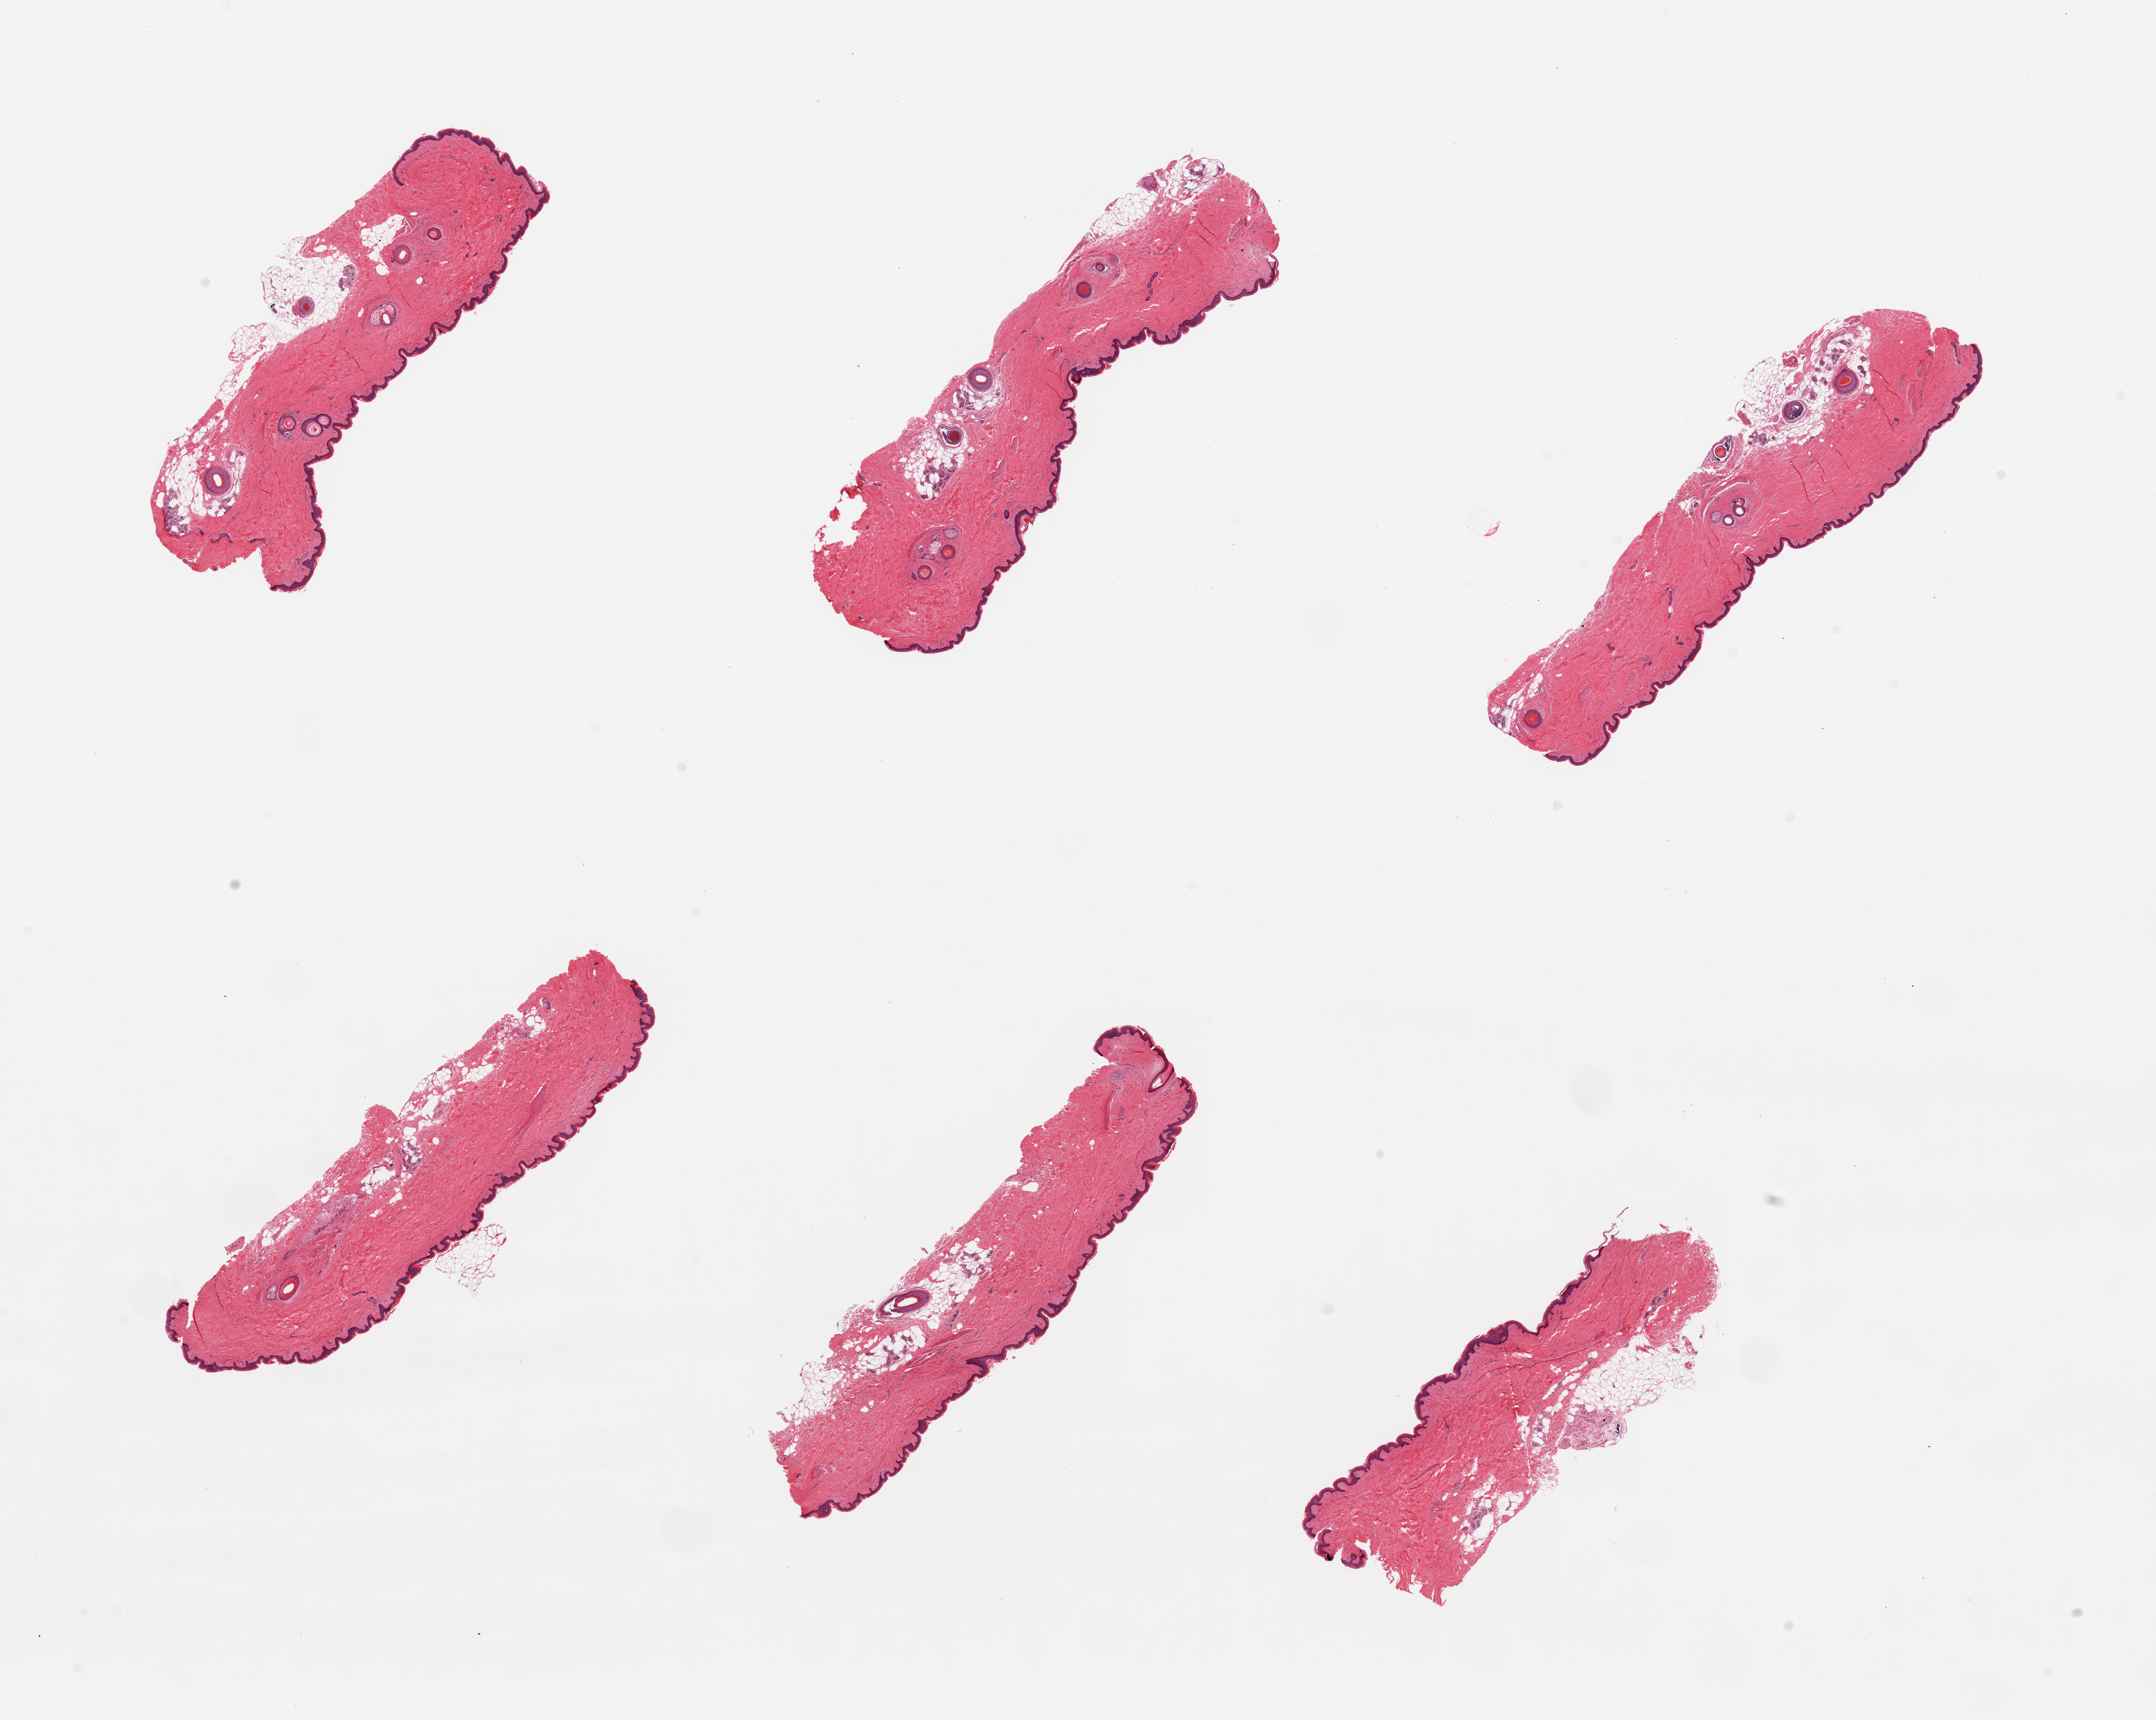
Haematoxylin and eosin whole-slide image — whole scanned area (about 24.6 x 19.6 mm) shown as a low-resolution overview; PAXgene-fixed, paraffin-embedded tissue; target tissue: skin of suprapubic region; tissue donor sample. Donor sex: female.
* pathologist's review note for this sample: 6 pieces; well trimmed deep surface; 20% intradermal fat; 2 have prominent hair follicles